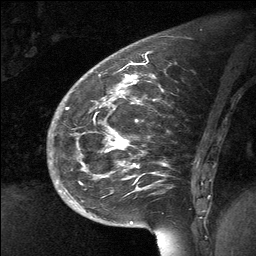
Breast MRI (dynamic contrast-enhanced), one sagittal slice; position 22 of 64 along the scan axis; dynamic contrast-enhanced study with each time point stored as its own series, time point 2 of 3 at this slice position (early post-contrast, ordered by acquisition time); 1.5 T; TE 4.8 ms, TR 27 ms; 256 × 256 image matrix, field of view 200 × 200 mm. Patient: female, 39 years. Case-level facts recorded for this patient, not image findings: setting: breast cancer imaged before/during neoadjuvant chemotherapy; receptor status: HER2-positive.
Structures marked on this image (semi-automatic segmentation, software-assisted and operator-edited):
- analysis volume of interest (the breast-tissue region the enhancement analysis was run in; not a lesion): bounding box [x1, y1, x2, y2] px = [70, 69, 202, 224]
- tumour enhancement mask (voxels above the 90 % enhancement threshold inside the analysis volume of interest): [106, 76, 138, 167]